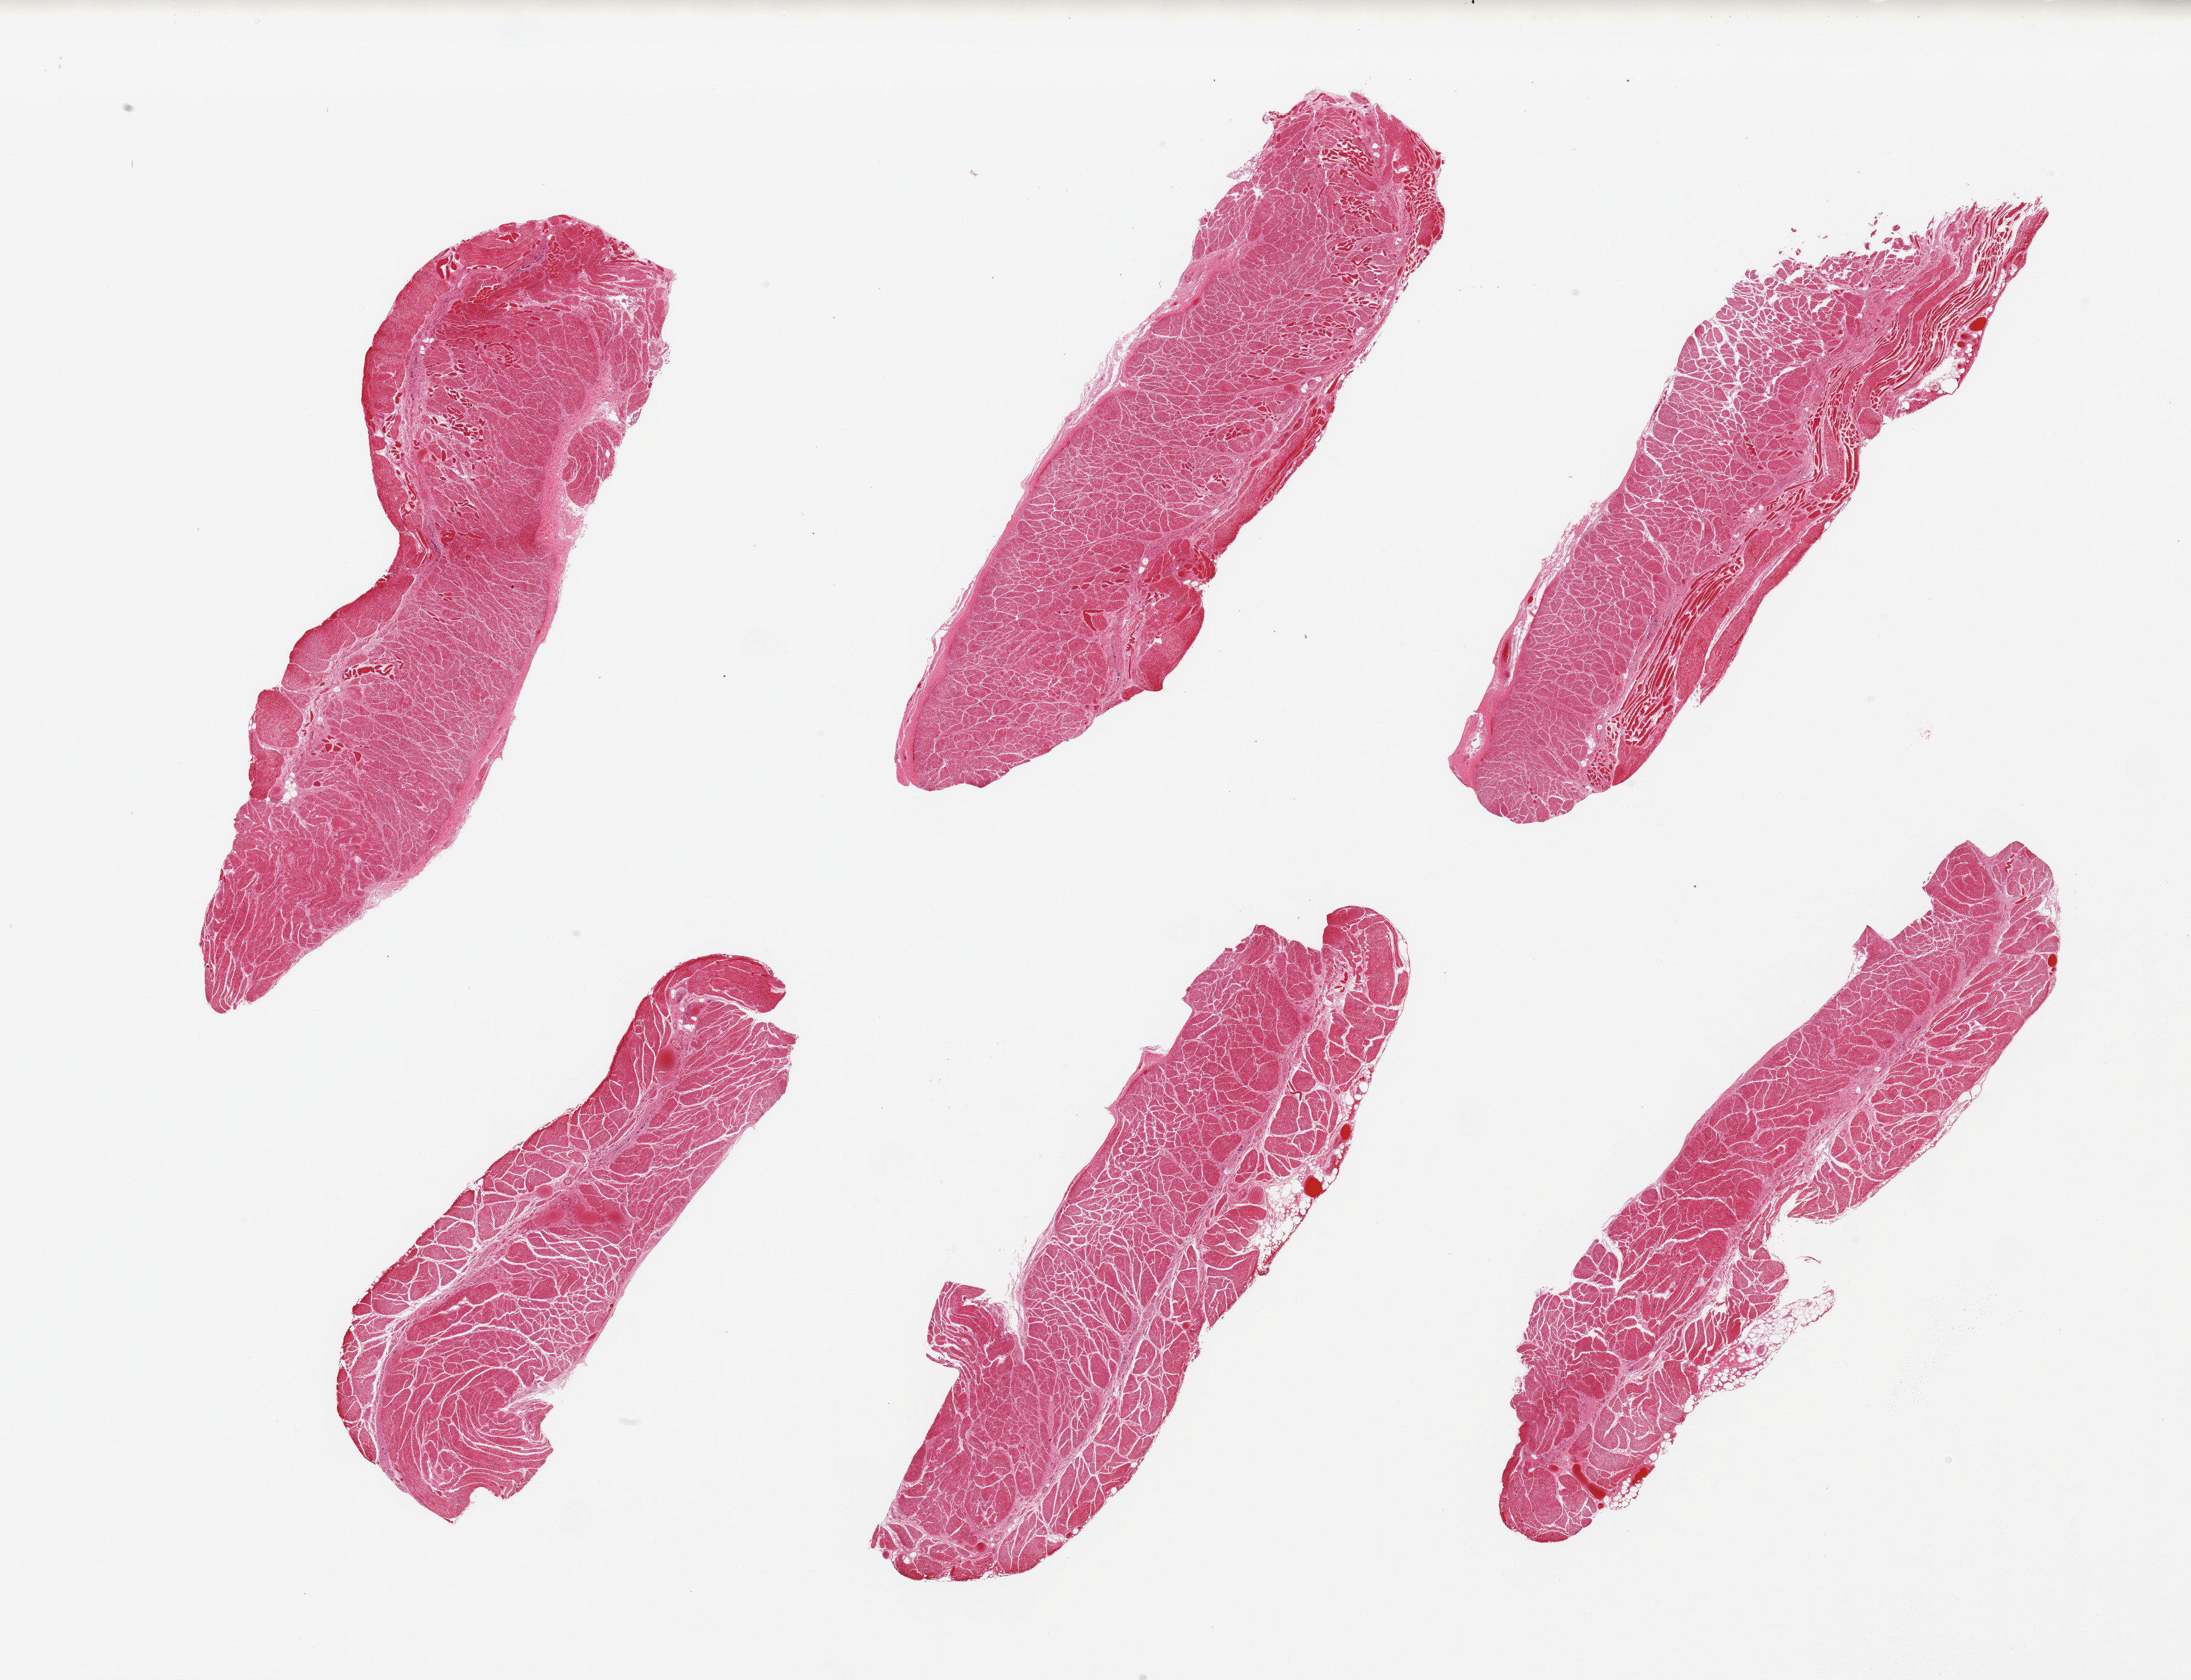
Digitized hematoxylin and eosin (H&E)-stained section, low-resolution overview of the scanned area, about 28.5 x 21.9 mm (acquisition: 20x scan), PAXgene-fixed paraffin-embedded (PFPE) section, target tissue: esophageal muscle, donor tissue sample. Donor: male.
Reviewer comment on this tissue sample: 6 pieces, confirmed target muscularis; myenteric plexus ganglion cells well-seen.